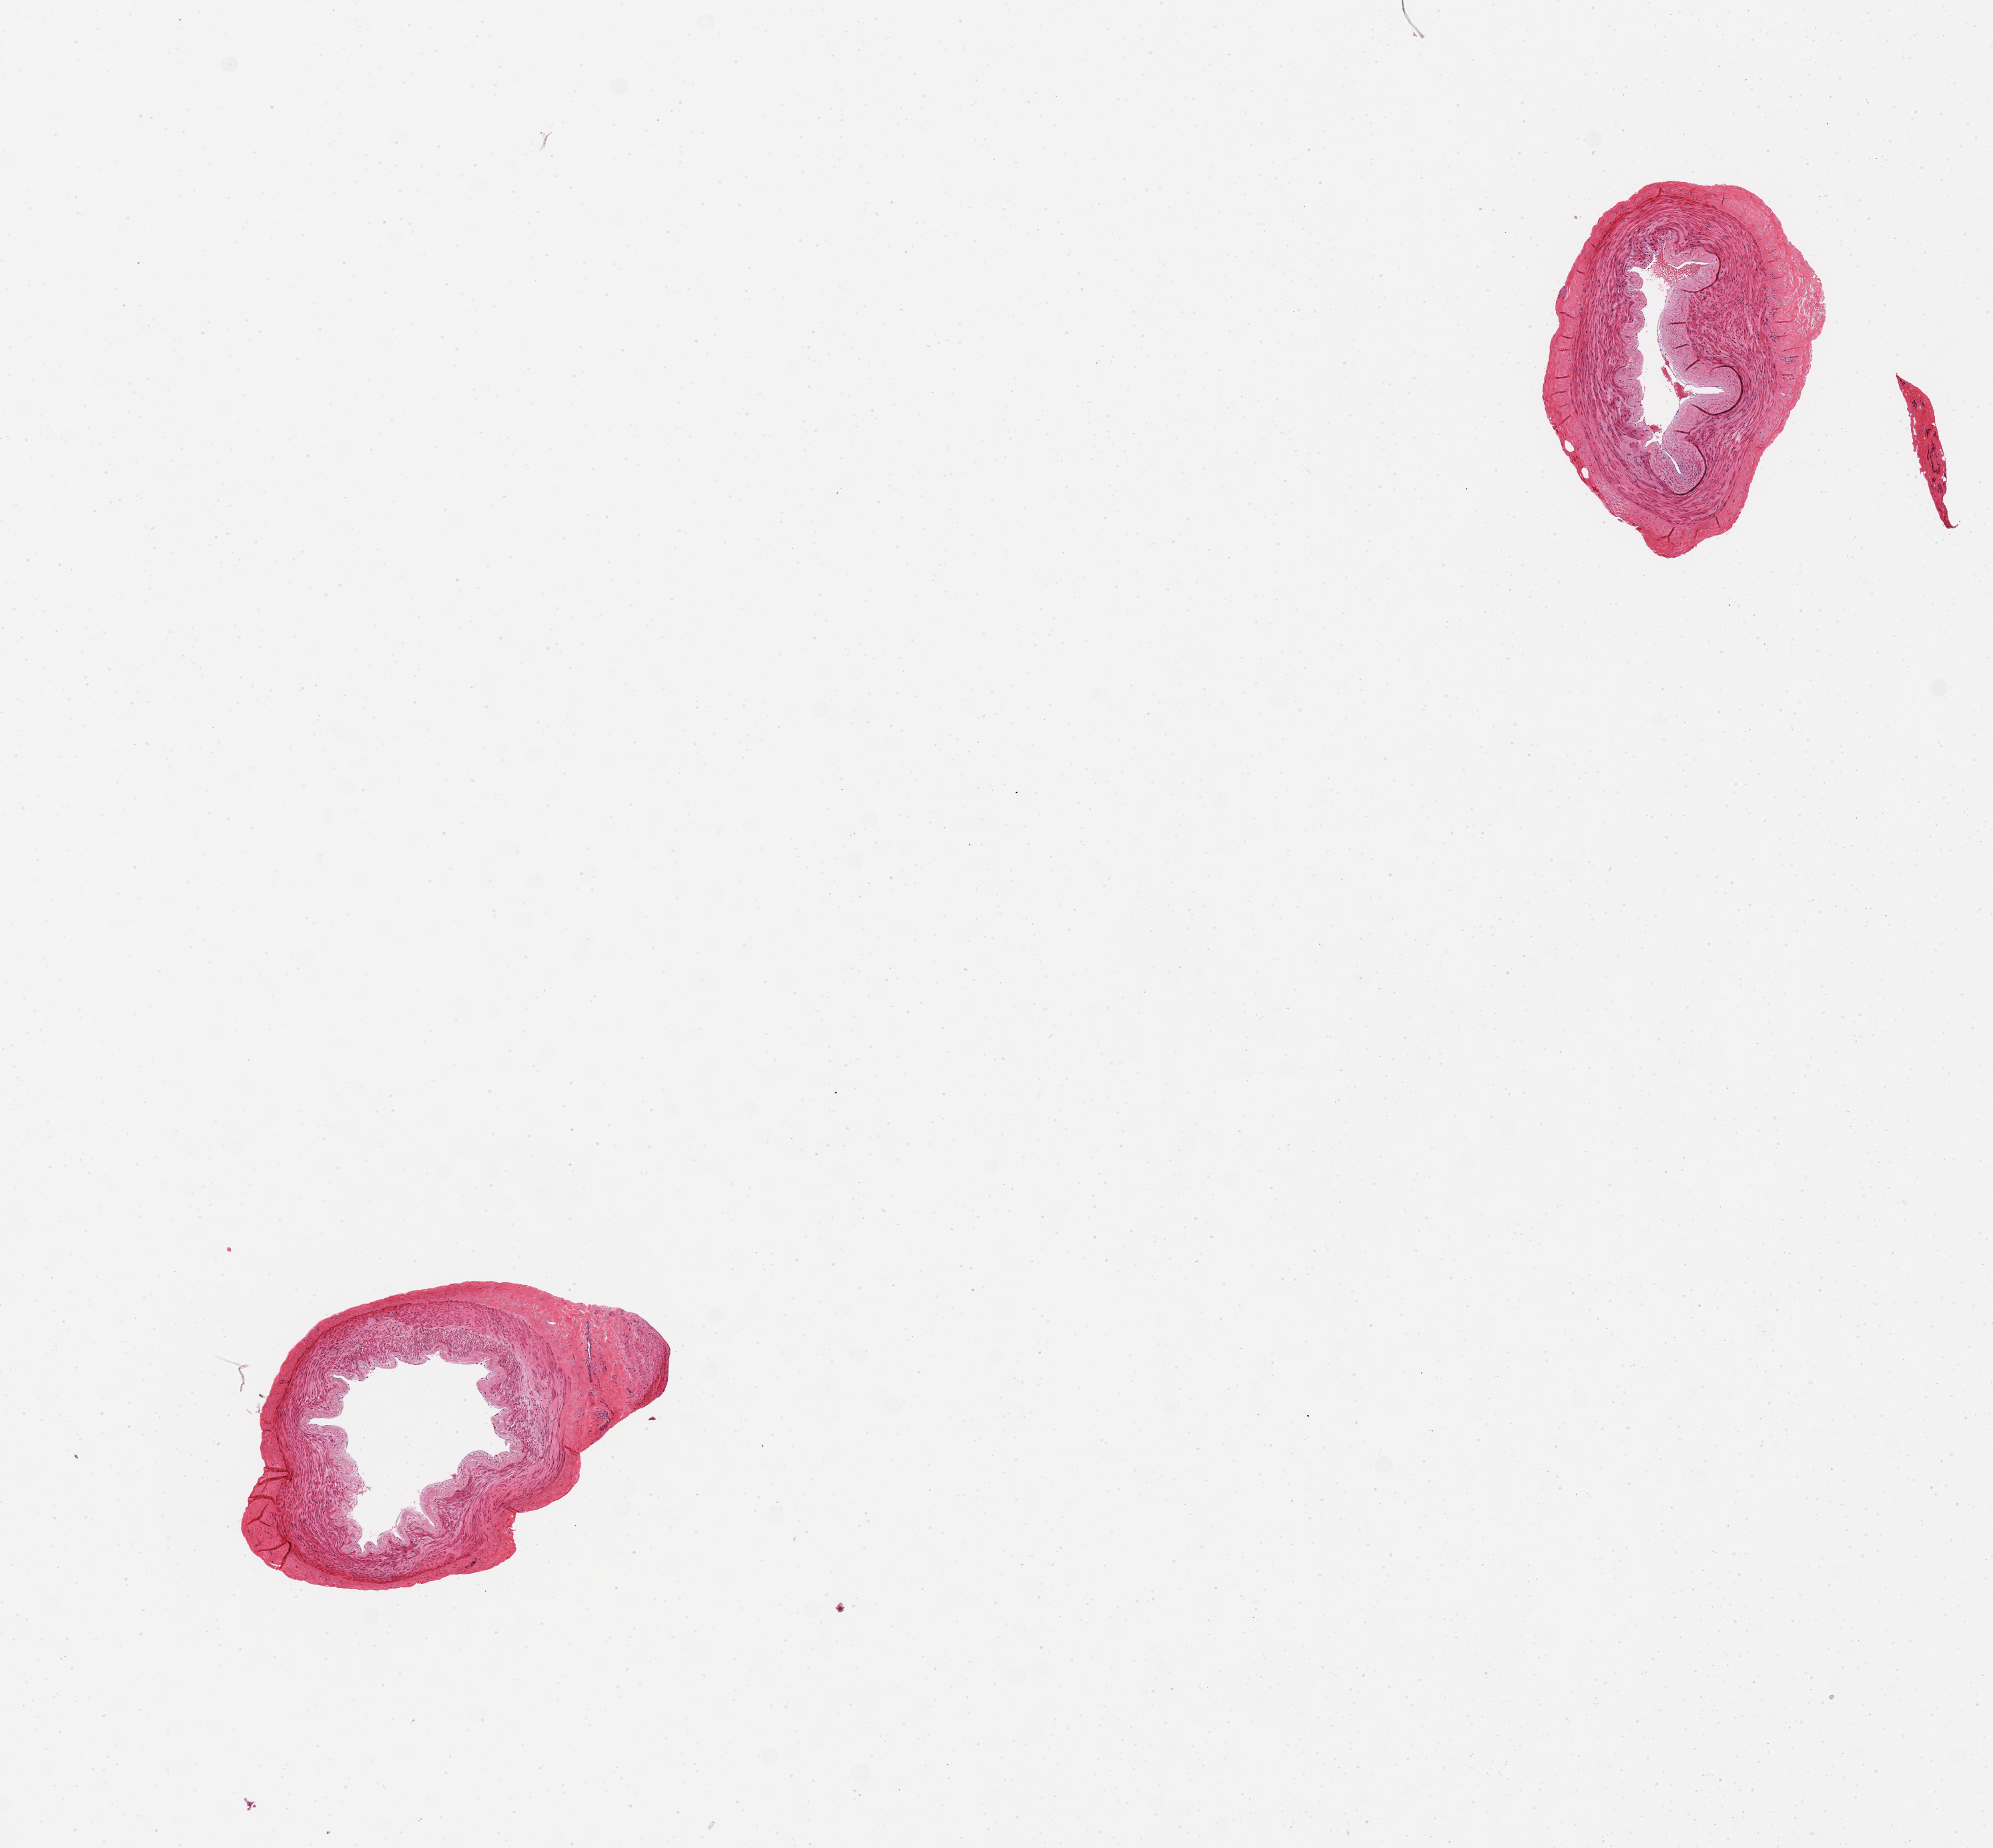
Whole-slide image, hematoxylin and eosin (H&E) stain, low-resolution overview of the scanned area, about 11.8 x 11.0 mm. PAXgene-fixed paraffin-embedded (PFPE) section. Section of tibial artery (target tissue). Tissue donor sample. Donor sex: female.
Reviewer comment on this tissue sample: 2 pieces.